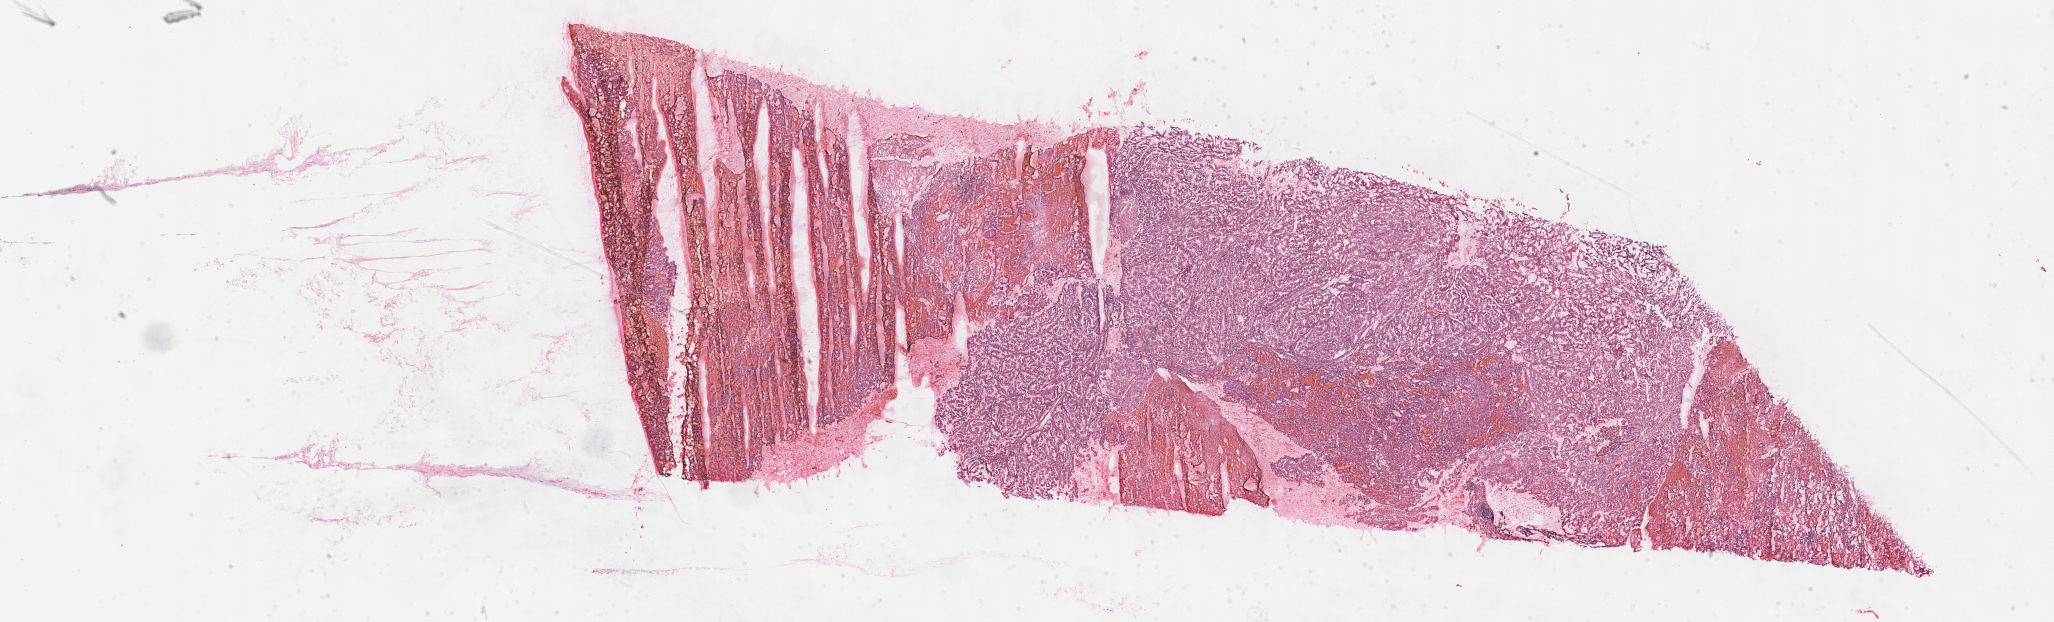
Whole-slide histology image, H&E, a low-resolution overview of the entire scanned area, about 33.2 x 10.1 mm (slide scanned at 40x). Formalin-fixed paraffin-embedded (FFPE) diagnostic section. Sample: primary tumour, kidney. Male patient. Histologic grade: G3 (poorly differentiated).
* TNM: T1a NX M0
* laterality: left
* pathologic diagnosis: Clear cell adenocarcinoma, NOS
* AJCC pathologic stage: I